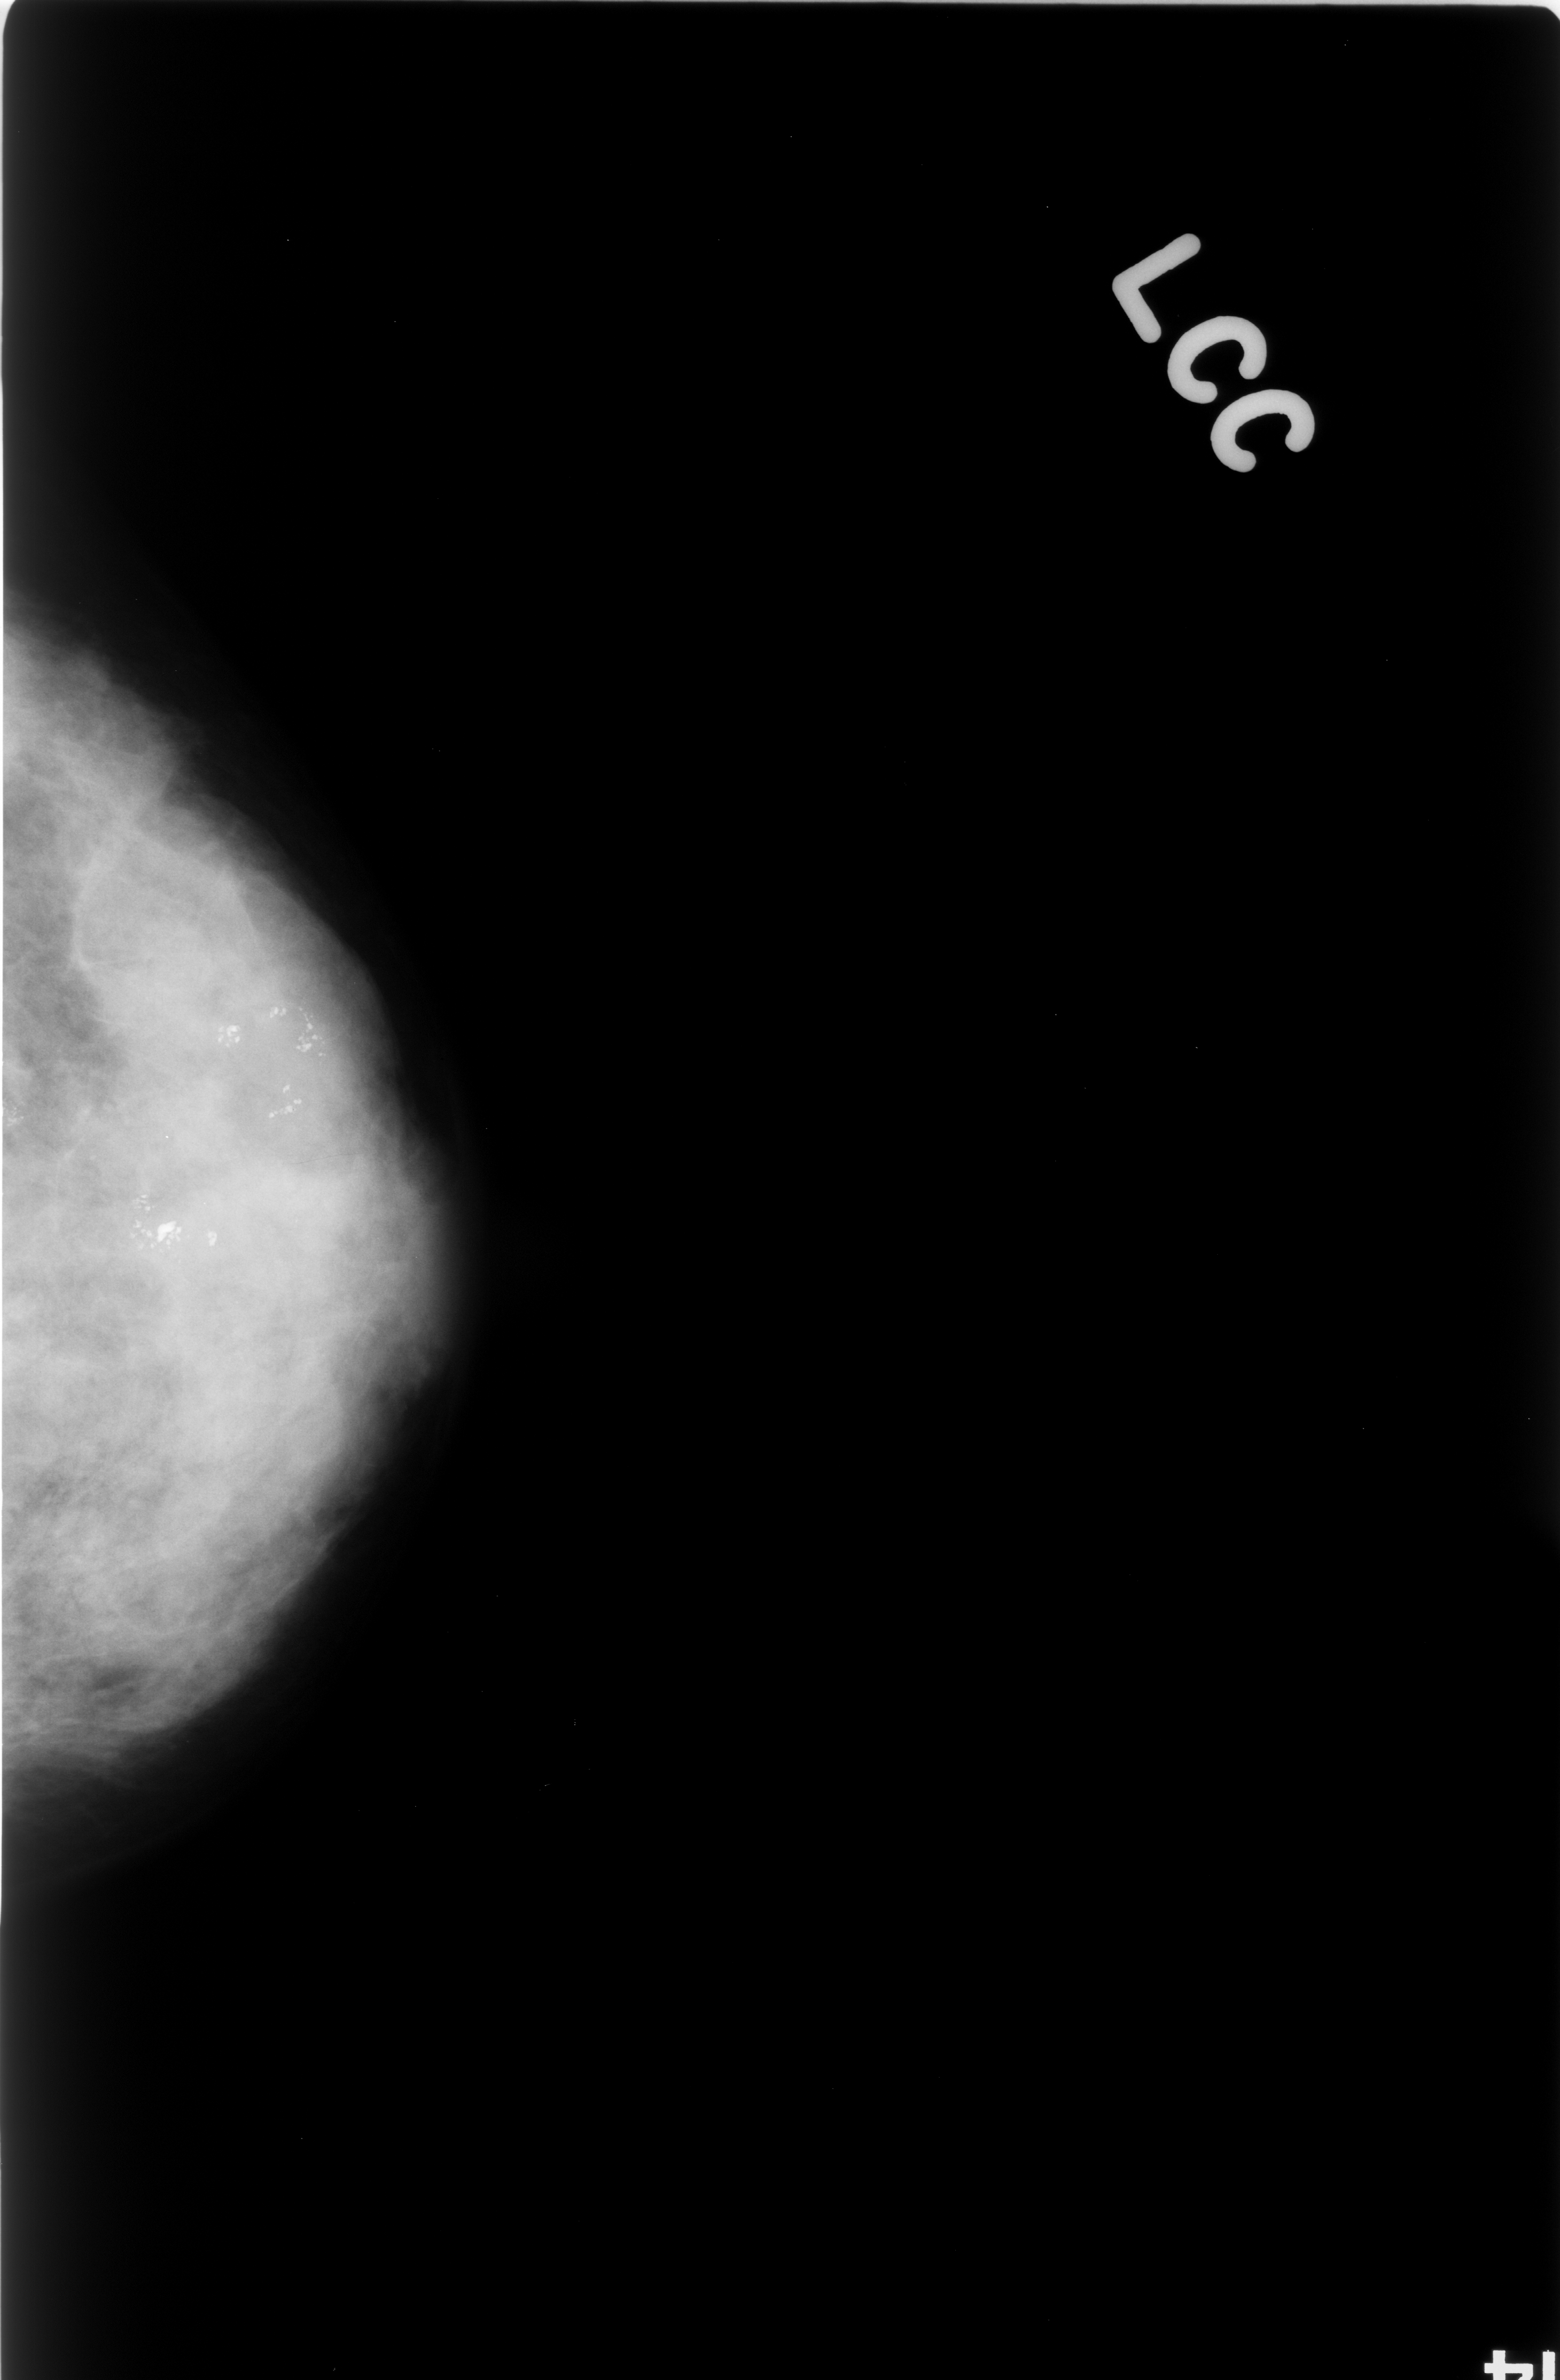
Digitized screen-film mammogram; left breast; craniocaudal (CC) view; BI-RADS breast density category 4 (scale 1–4).
Radiologist-marked abnormalities on this image: Finding 1 of 3: calcifications, morphology pleomorphic, distribution clustered; BI-RADS assessment category 4; subtlety rating 5 on a 1 (subtle) to 5 (obvious) scale; pathology (as recorded): benign. Finding 2 of 3: calcifications, morphology pleomorphic, distribution clustered; BI-RADS assessment category 4; pathology (as recorded): benign. Finding 3 of 3: calcifications, morphology pleomorphic, distribution clustered; BI-RADS assessment category 4; pathology result (as recorded, not read from the image): benign.